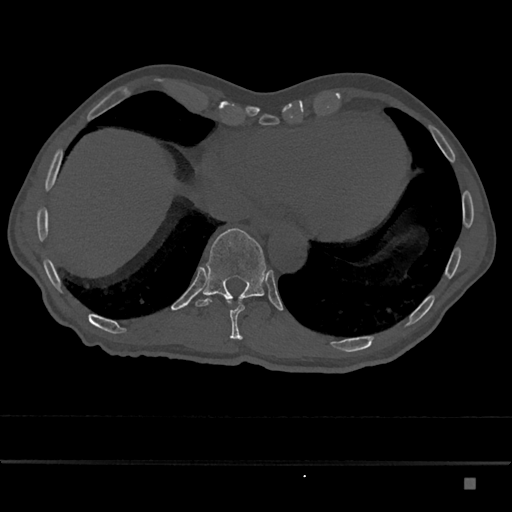
CT including the spine, one axial slice; position 706 of 797 along the scan axis; reconstruction kernel Br40s/3; 120 kVp; bone window (W 1800 / L 400 HU); 512 × 512 image matrix. Patient: male, 72 years. From the clinical record (not read from this slice): primary cancer: prostate.
Outlined on this slice (semi-automatic segmentation, software-assisted and operator-edited):
- T10 vertebra: box from (x=226, y=298) to (x=245, y=340) px
- T11 vertebra: (x=195, y=228)–(x=267, y=307)